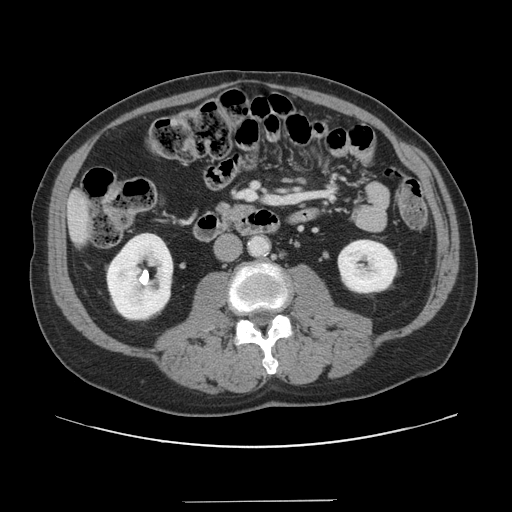
Contrast-enhanced abdominal CT, one axial slice; slice 38 of 151 in the series (ordered by position); 120 kVp; intravenous contrast given; soft-tissue window (W 400 / L 40 HU); 2.5 mm slice thickness; 512 × 512 image matrix, field of view 399 × 399 mm. Male patient, age 63 years. Case-level facts recorded for this patient, not image findings: diagnosis: colorectal cancer liver metastases, imaged before liver resection; multiple liver metastases: no; largest metastasis: 2.1 cm; disease in both lobes: no.
Outlined on this slice (outlined manually by an expert reader):
- liver: box from (x=69, y=193) to (x=91, y=243) px
- planned liver remnant (the part of the liver to remain after resection): (x=69, y=192)–(x=91, y=244)
- portal vein (with intrahepatic branches): (x=240, y=191)–(x=255, y=199)